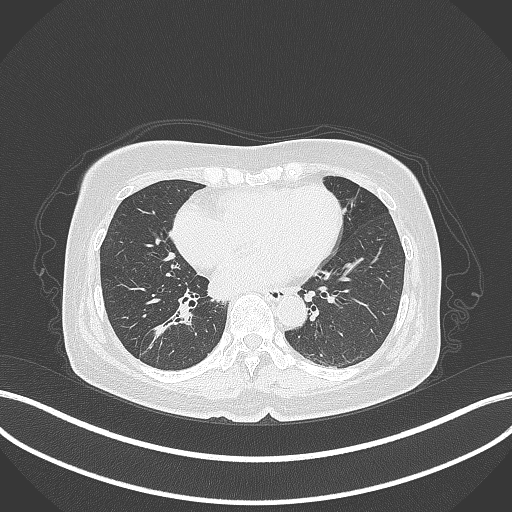
Chest CT, one axial slice. Position 164 of 429 along the scan axis. Lung window (W 1500 / L -600 HU). 1 mm slice thickness. 512 × 512 image matrix, field of view 400 × 400 mm. Patient: female, 67 years. Case-level facts recorded for this patient, not image findings: clinical TNM (as recorded): T1c N1 M0.
Outlined on this slice (bounding box drawn by a radiologist):
- lung tumour (recorded histology: adenocarcinoma): bounding box <140,300,197,349> (left, top, right, bottom; pixels)